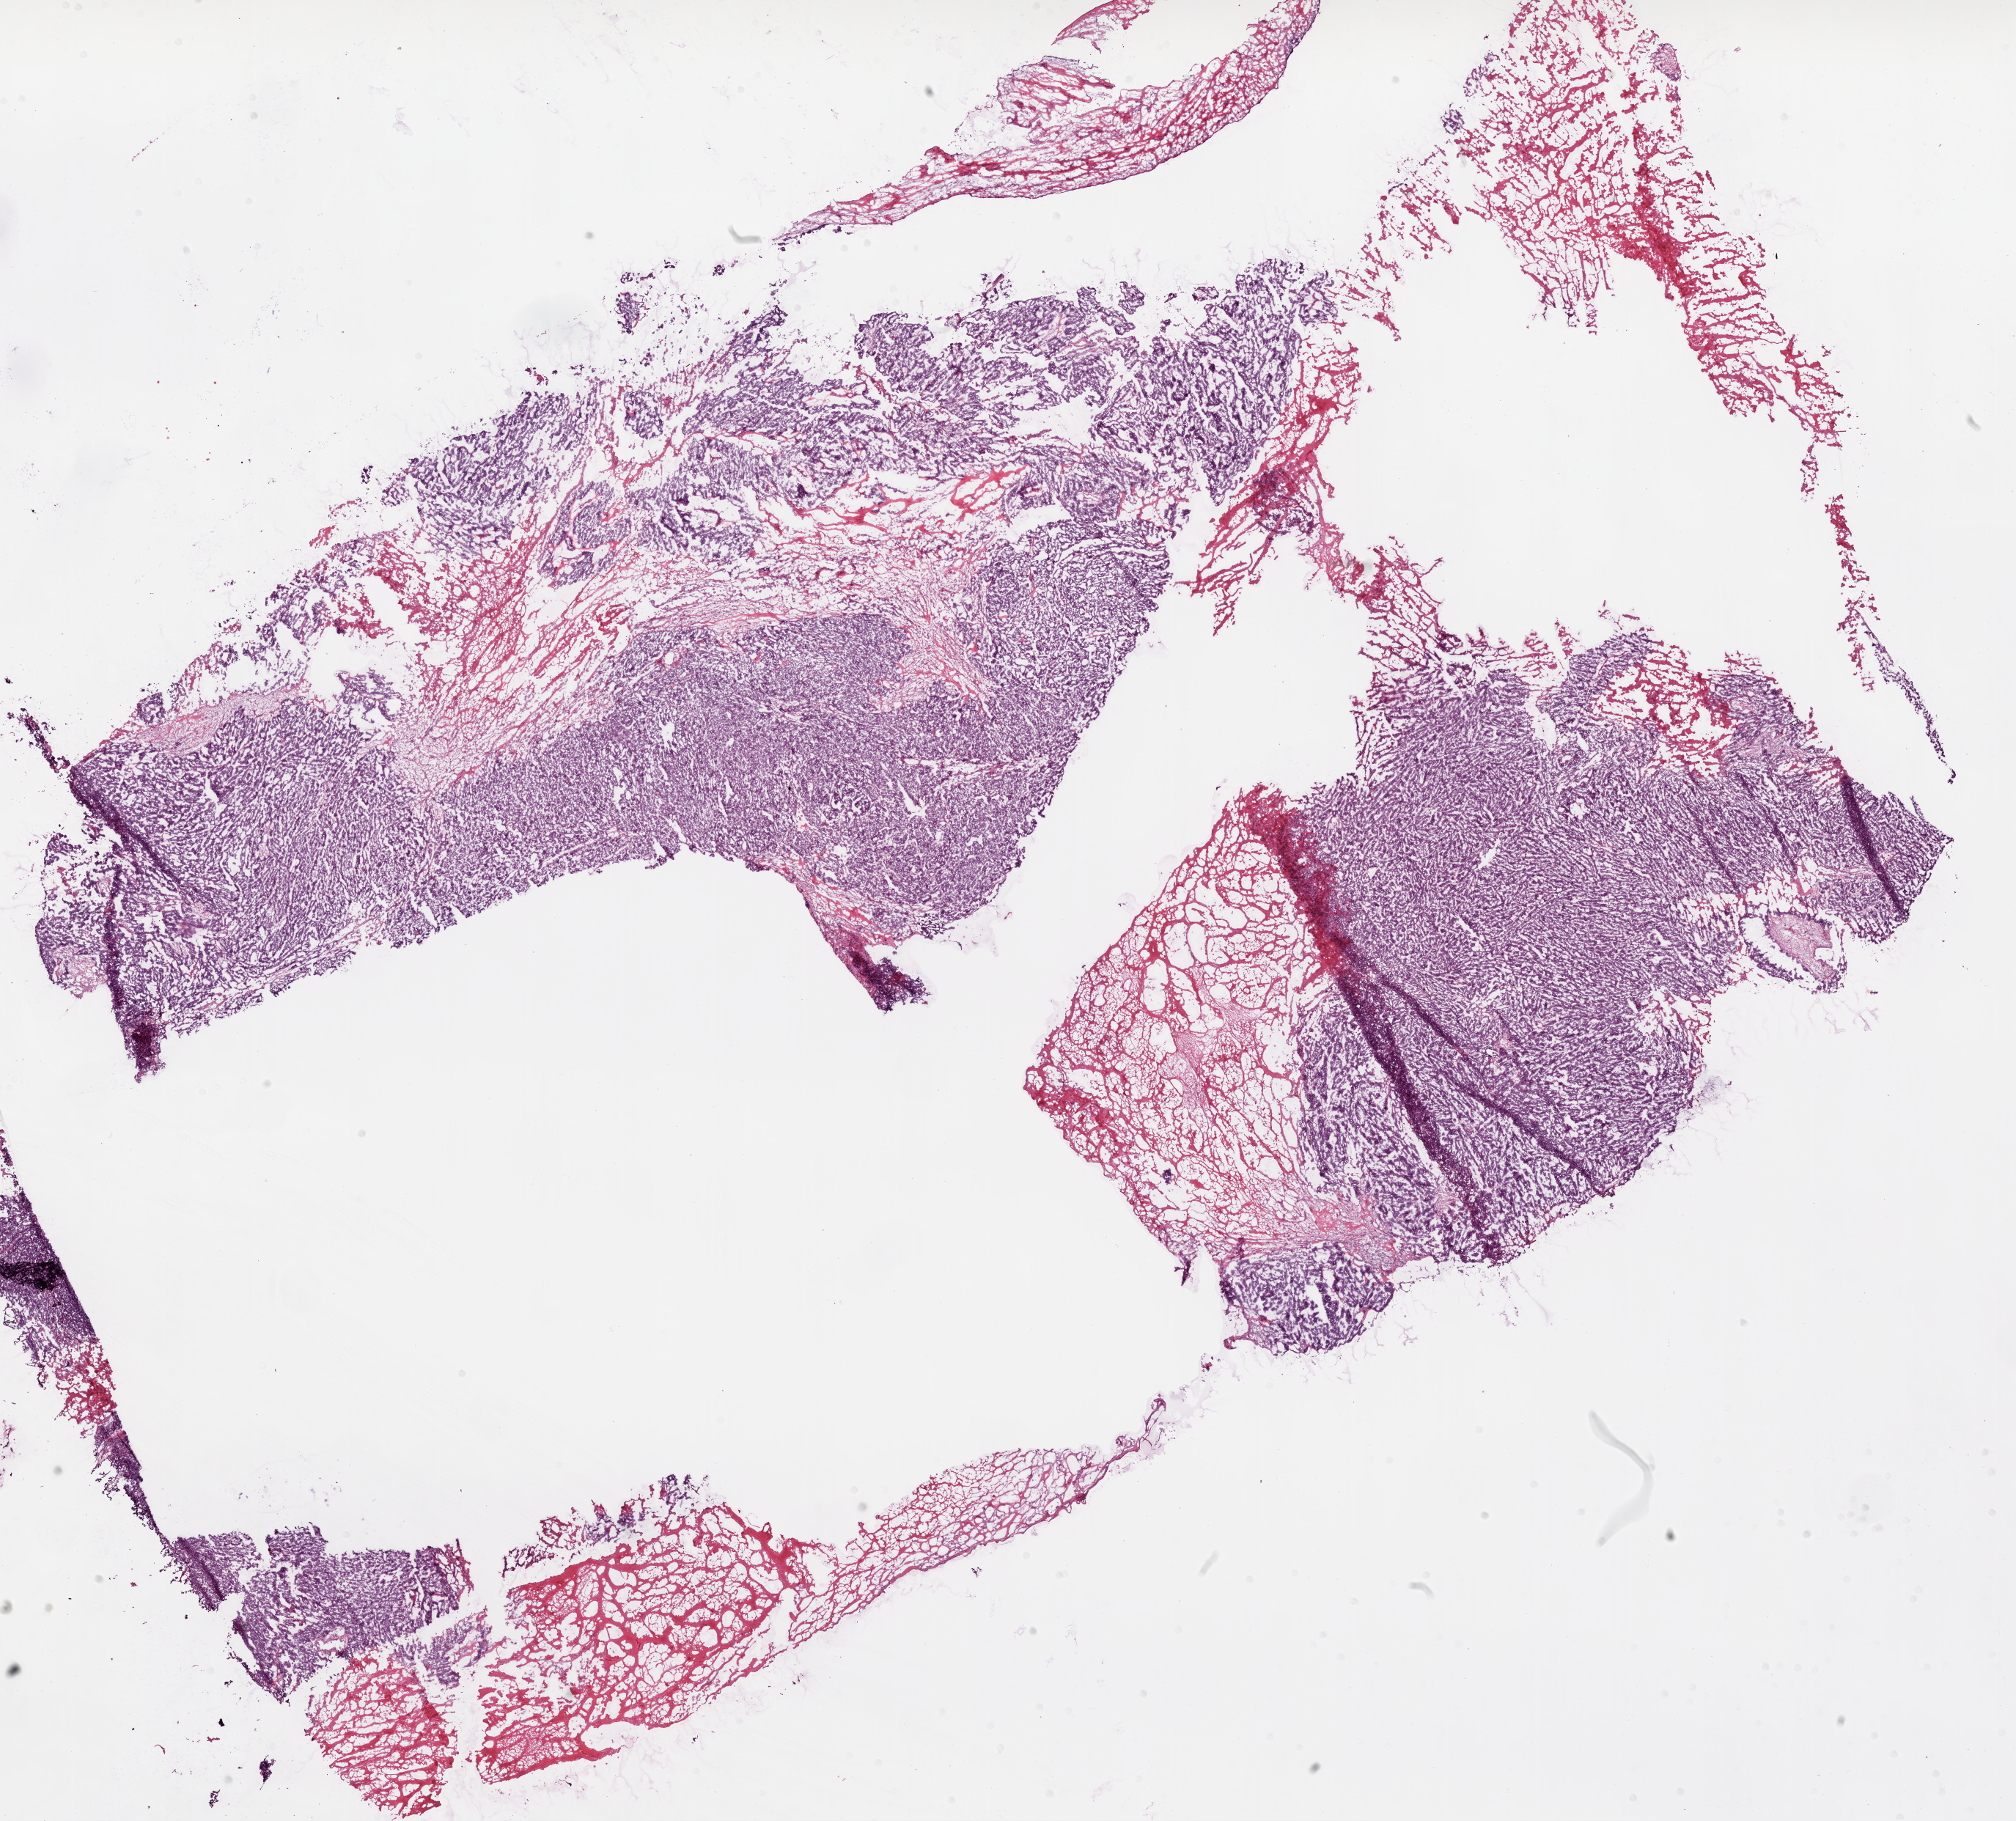
Whole-slide histology image, H&E-stained, shown as a low-resolution overview of the whole scanned area (about 22.1 x 19.9 mm, acquisition: 20x scan). Frozen section. Primary tumour sample from the ovary. Patient: female, age at initial diagnosis 62 years. Histologic grade: G3 (poorly differentiated). Composition of this section per pathologist review: tumour cells 75%, tumour nuclei 95%, normal cells 0%, stromal cells 5%, necrosis 20%.
- FIGO stage: IIIC
- laterality: left
- histologic diagnosis: Serous cystadenocarcinoma, NOS